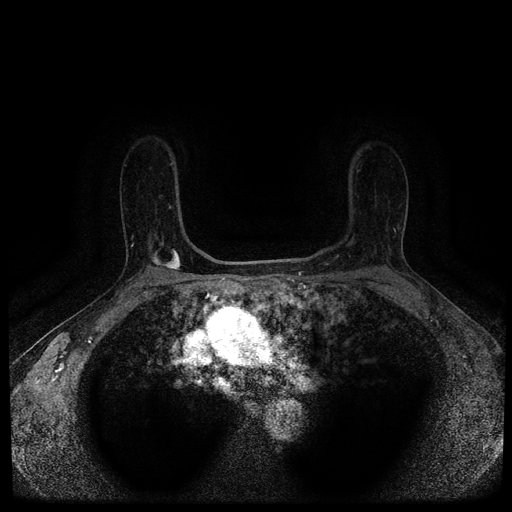
Breast MRI (dynamic contrast-enhanced, multi-phase), one axial slice; position 73 of 116 along the scan axis; dynamic contrast-enhanced series, time point 2 of 5 at this slice position (early post-contrast); 1.5 T; TE 2.7 ms, TR 5.4 ms; 2 mm slice thickness; 512 × 512 image matrix, field of view 330 × 330 mm. Patient: female, 63 years.
Annotated regions visible in this slice (semi-automatic segmentation, software-assisted and operator-edited):
- breast lesion (labelled 'tumour' in the annotation; benign lesions carry a separate 'benign' label): bounding box <150,248,183,272> (left, top, right, bottom; pixels)